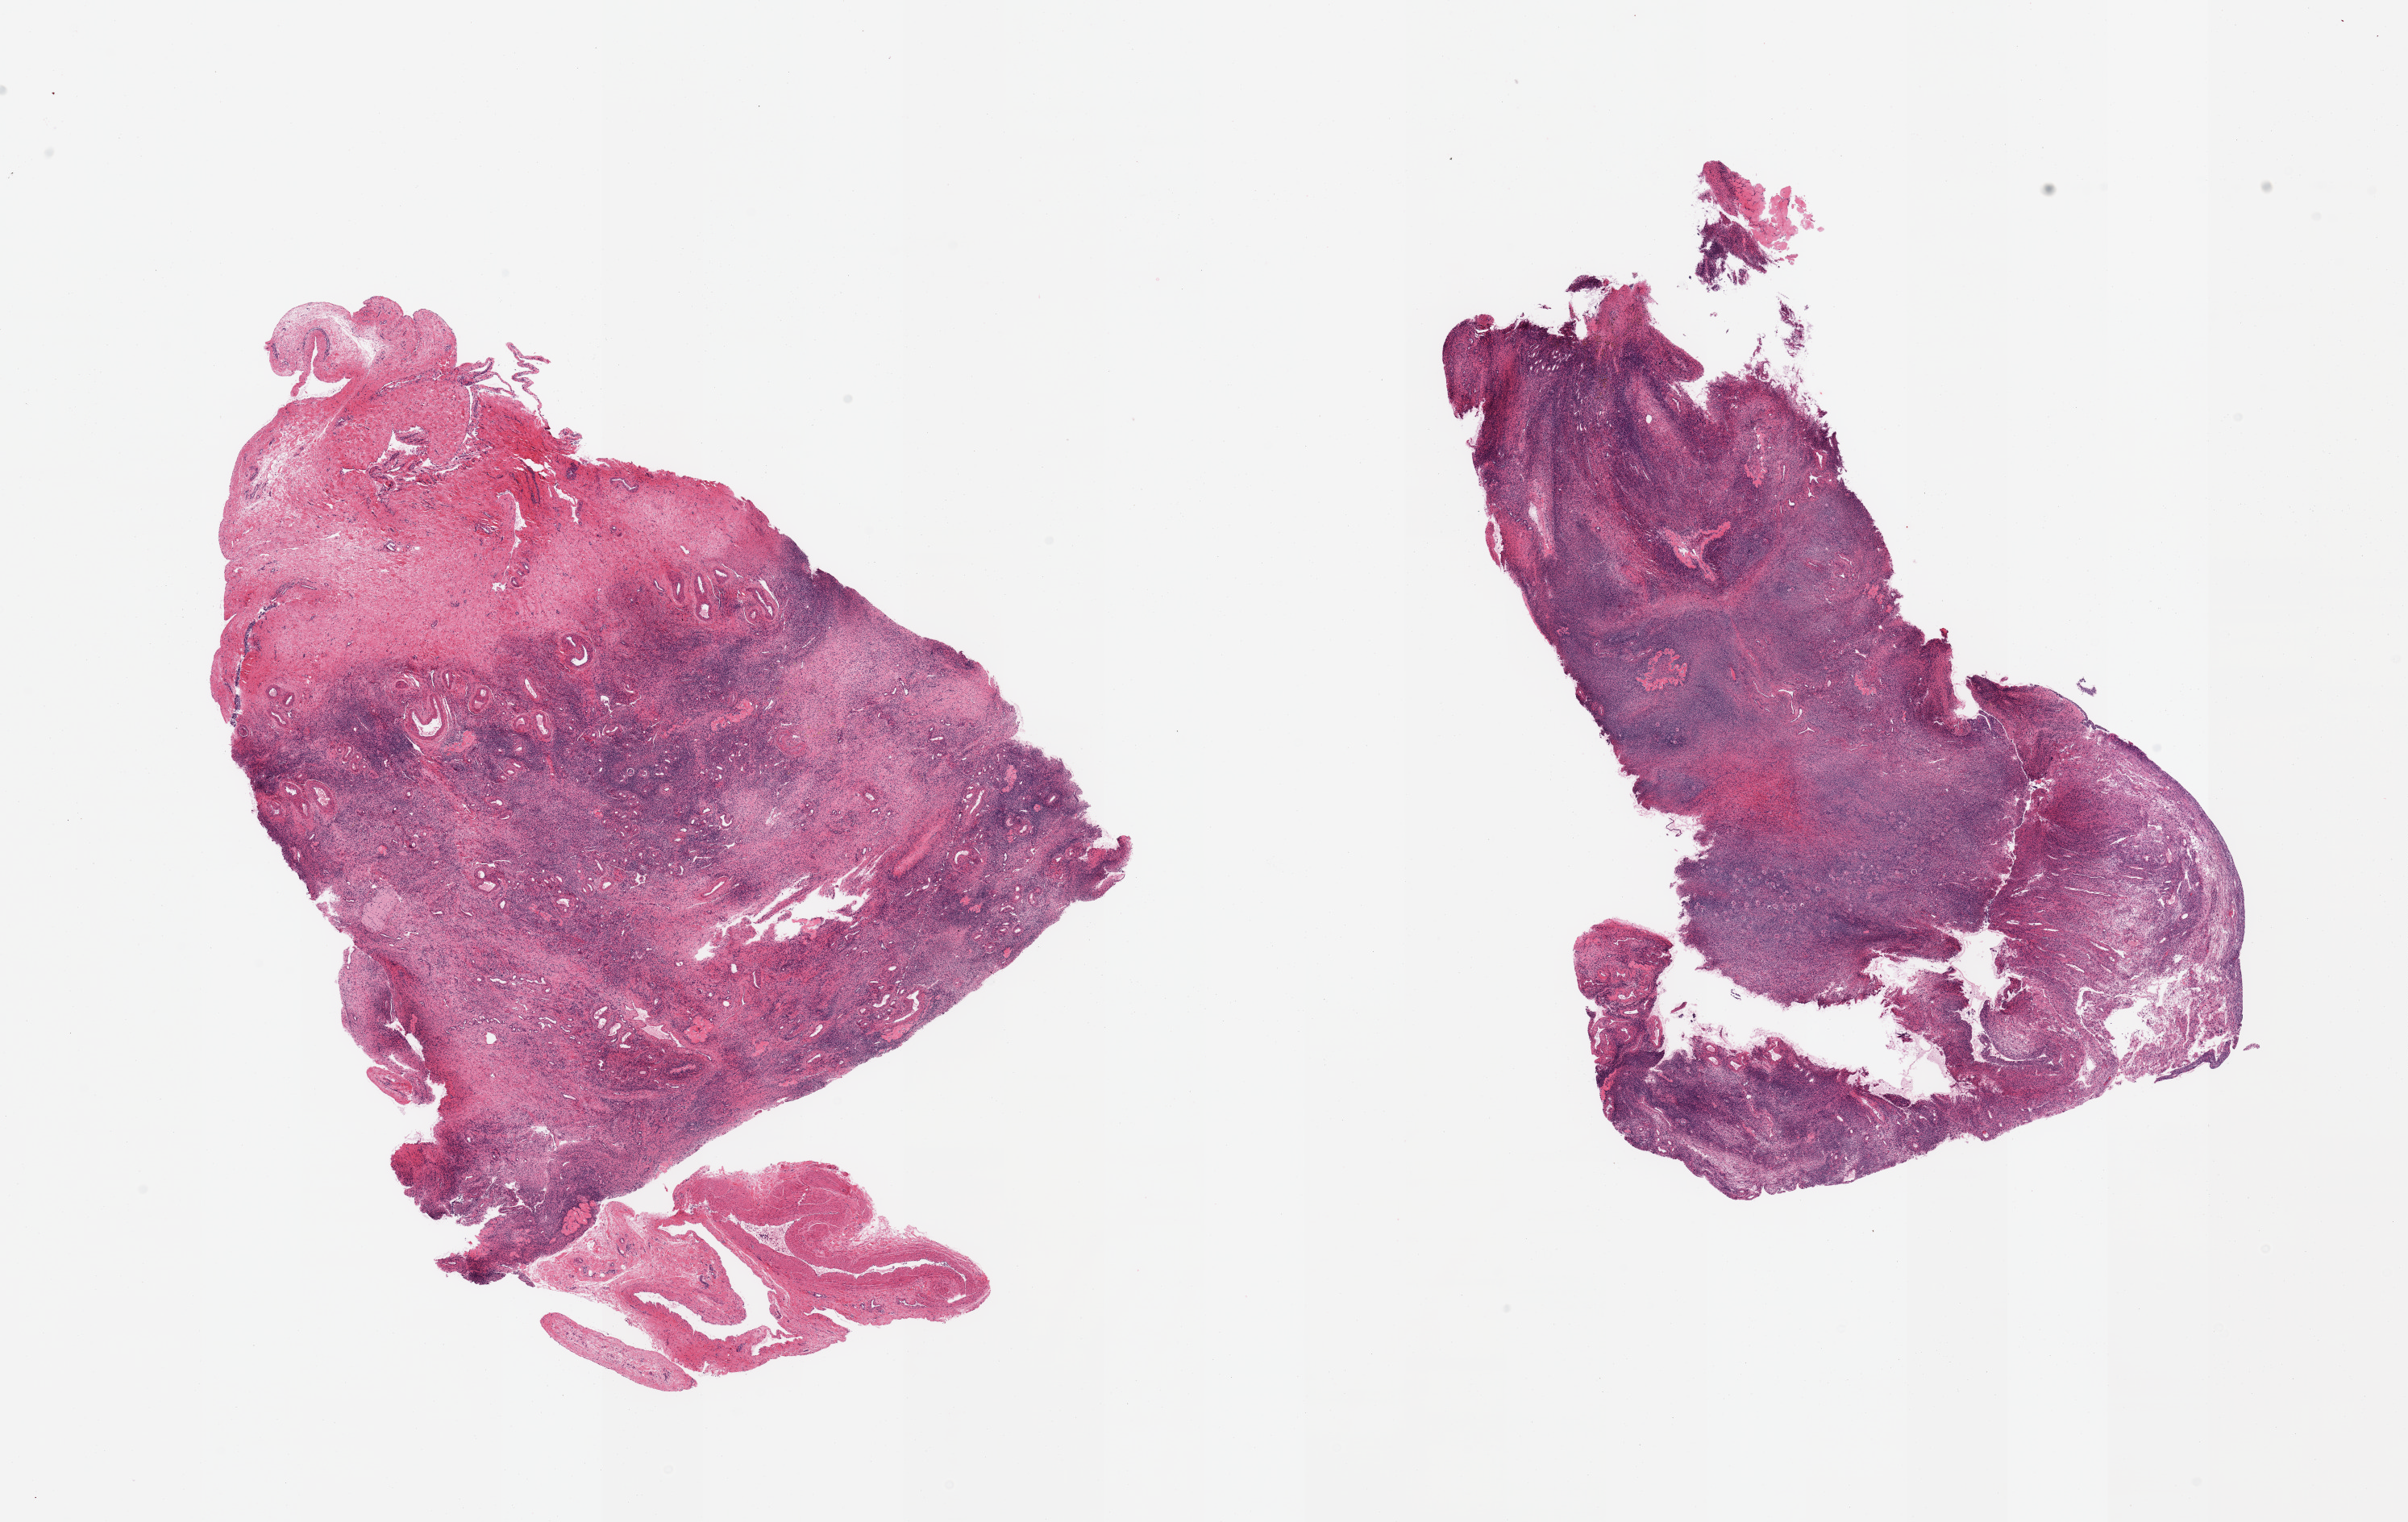
Haematoxylin and eosin whole-slide image, brightfield — shown as a low-resolution overview of the whole scanned area (about 23.6 x 14.9 mm); PAXgene-fixed, paraffin-embedded tissue; sampled site (target tissue): ovary; tissue donor sample. Female donor.
Review note (as recorded): 2 pieces; ovarian stroma with follicles; vascular accentuation.